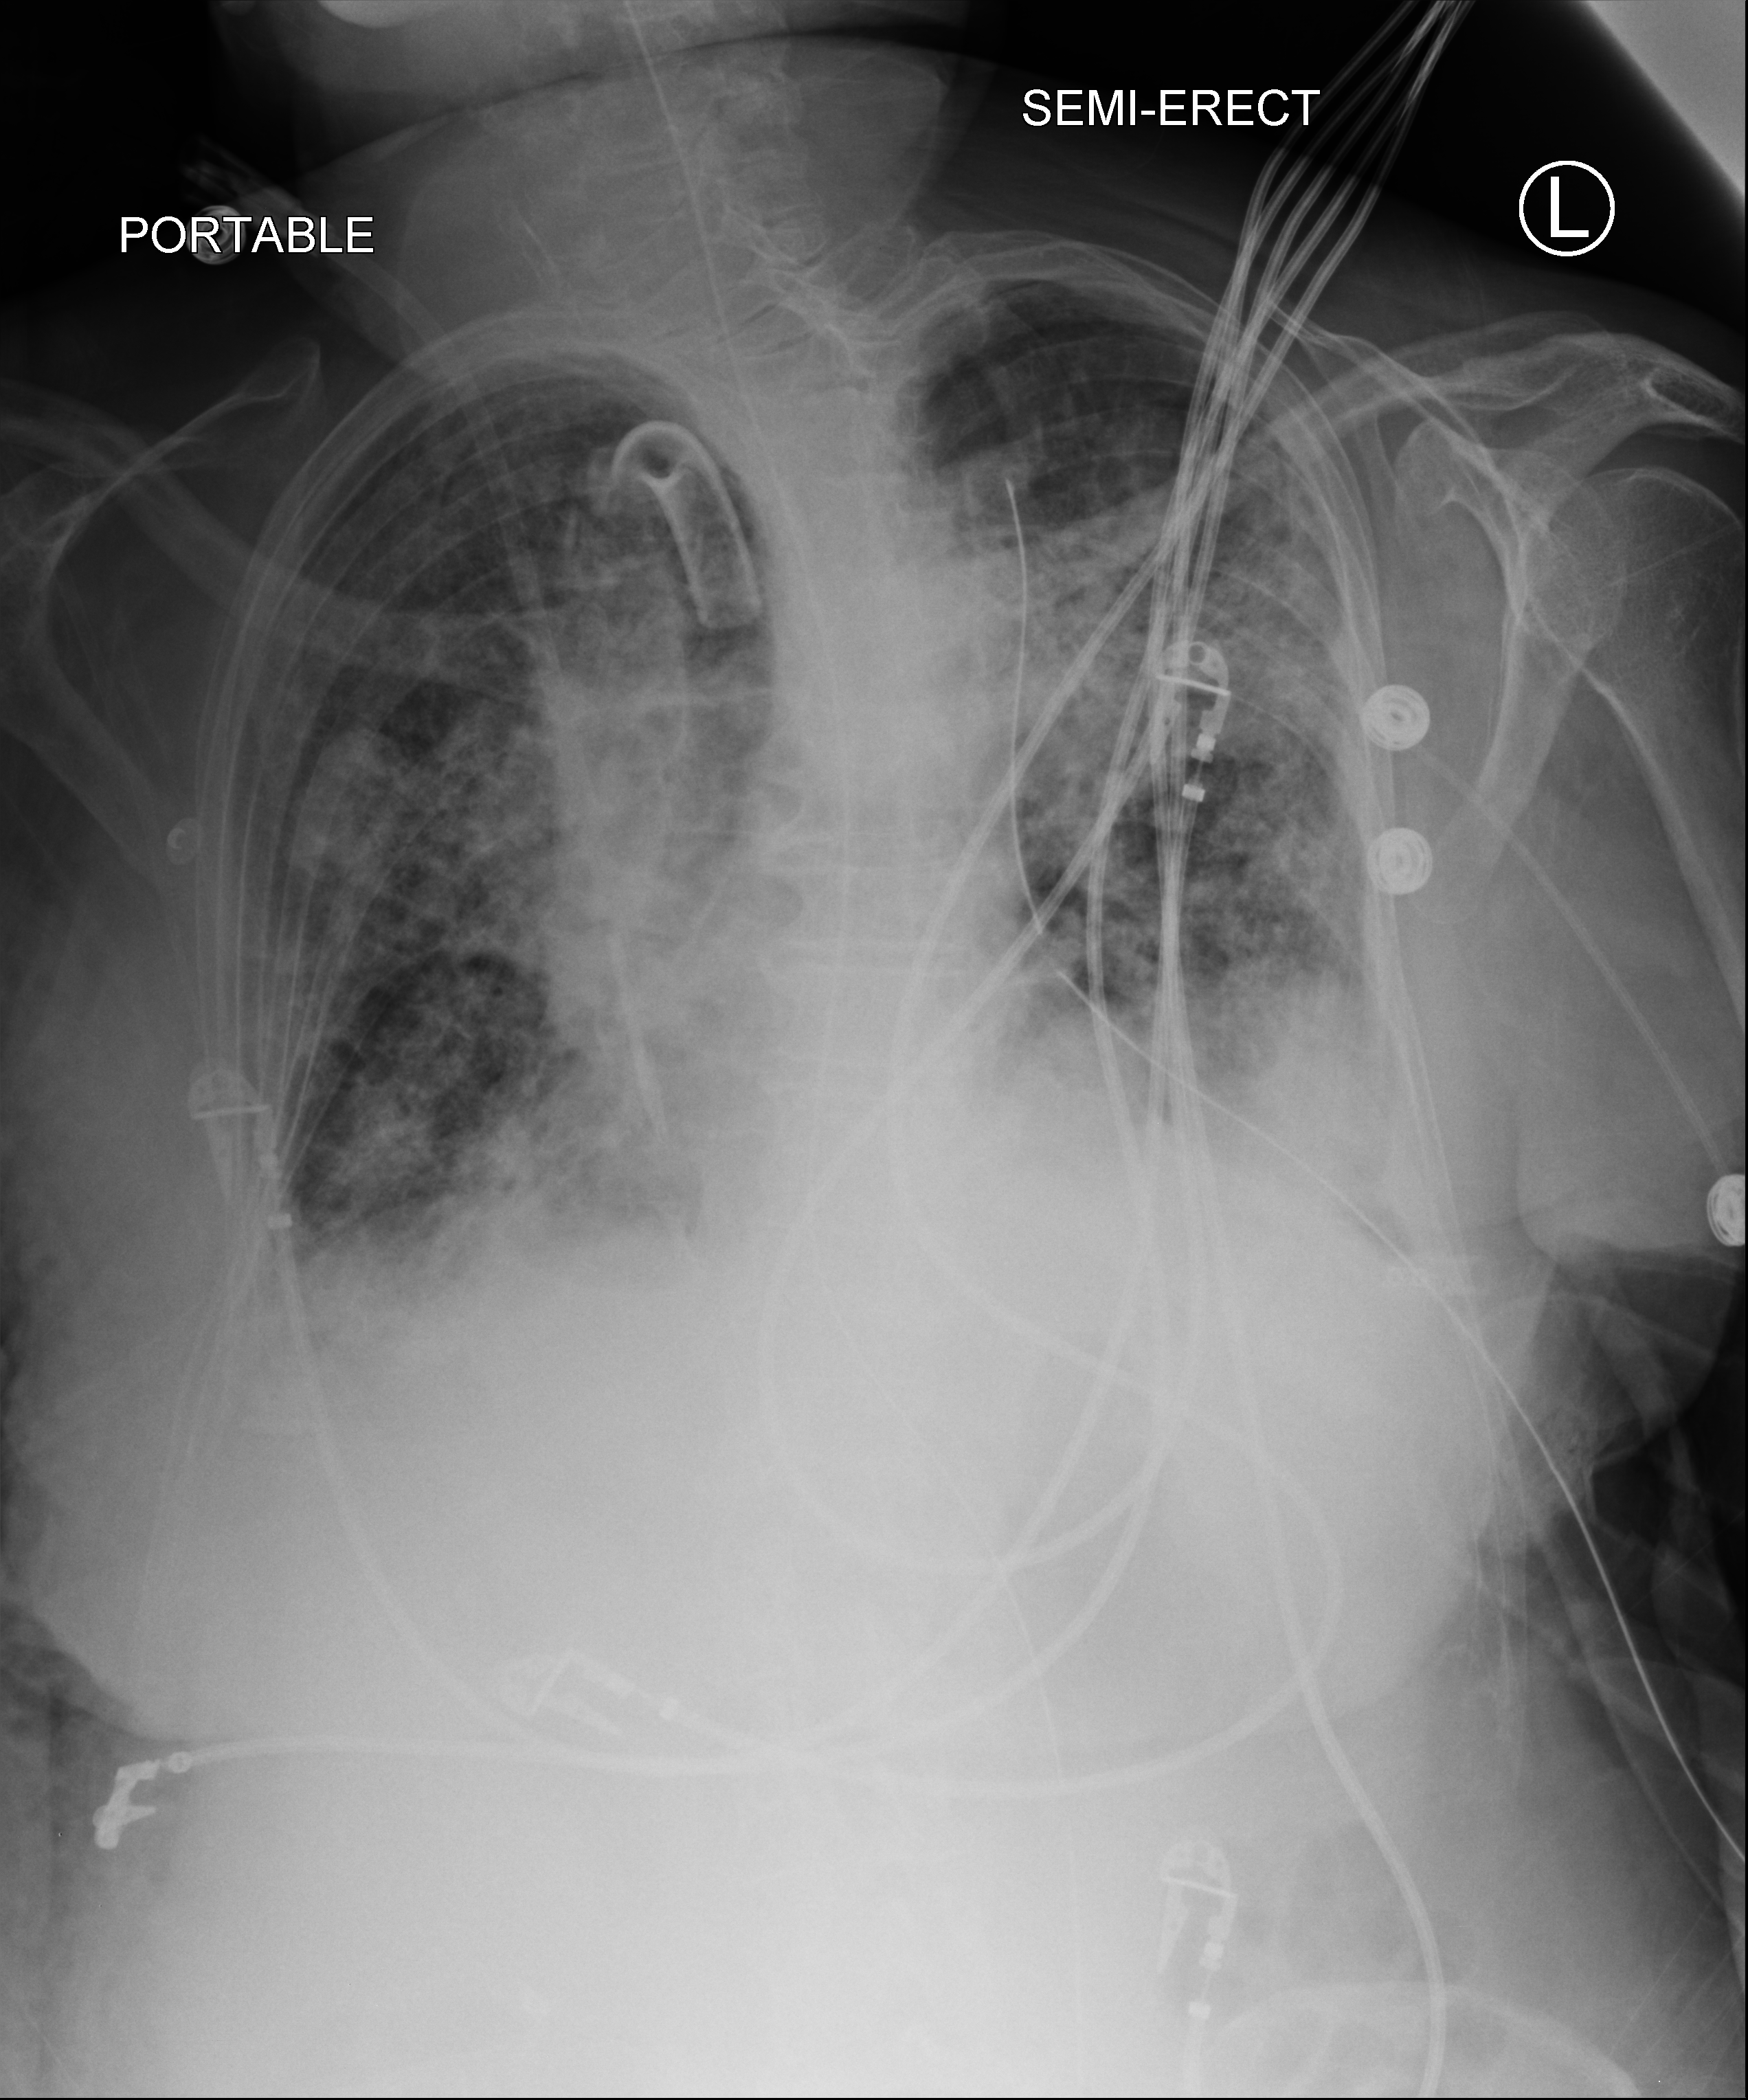
Portable chest radiograph. Female patient hospitalised with COVID-19, age 75–90 years.
Hospital-stay facts (about this admission, not read from this image; timing relative to this image not recorded):
- chronic kidney disease (admission record): no